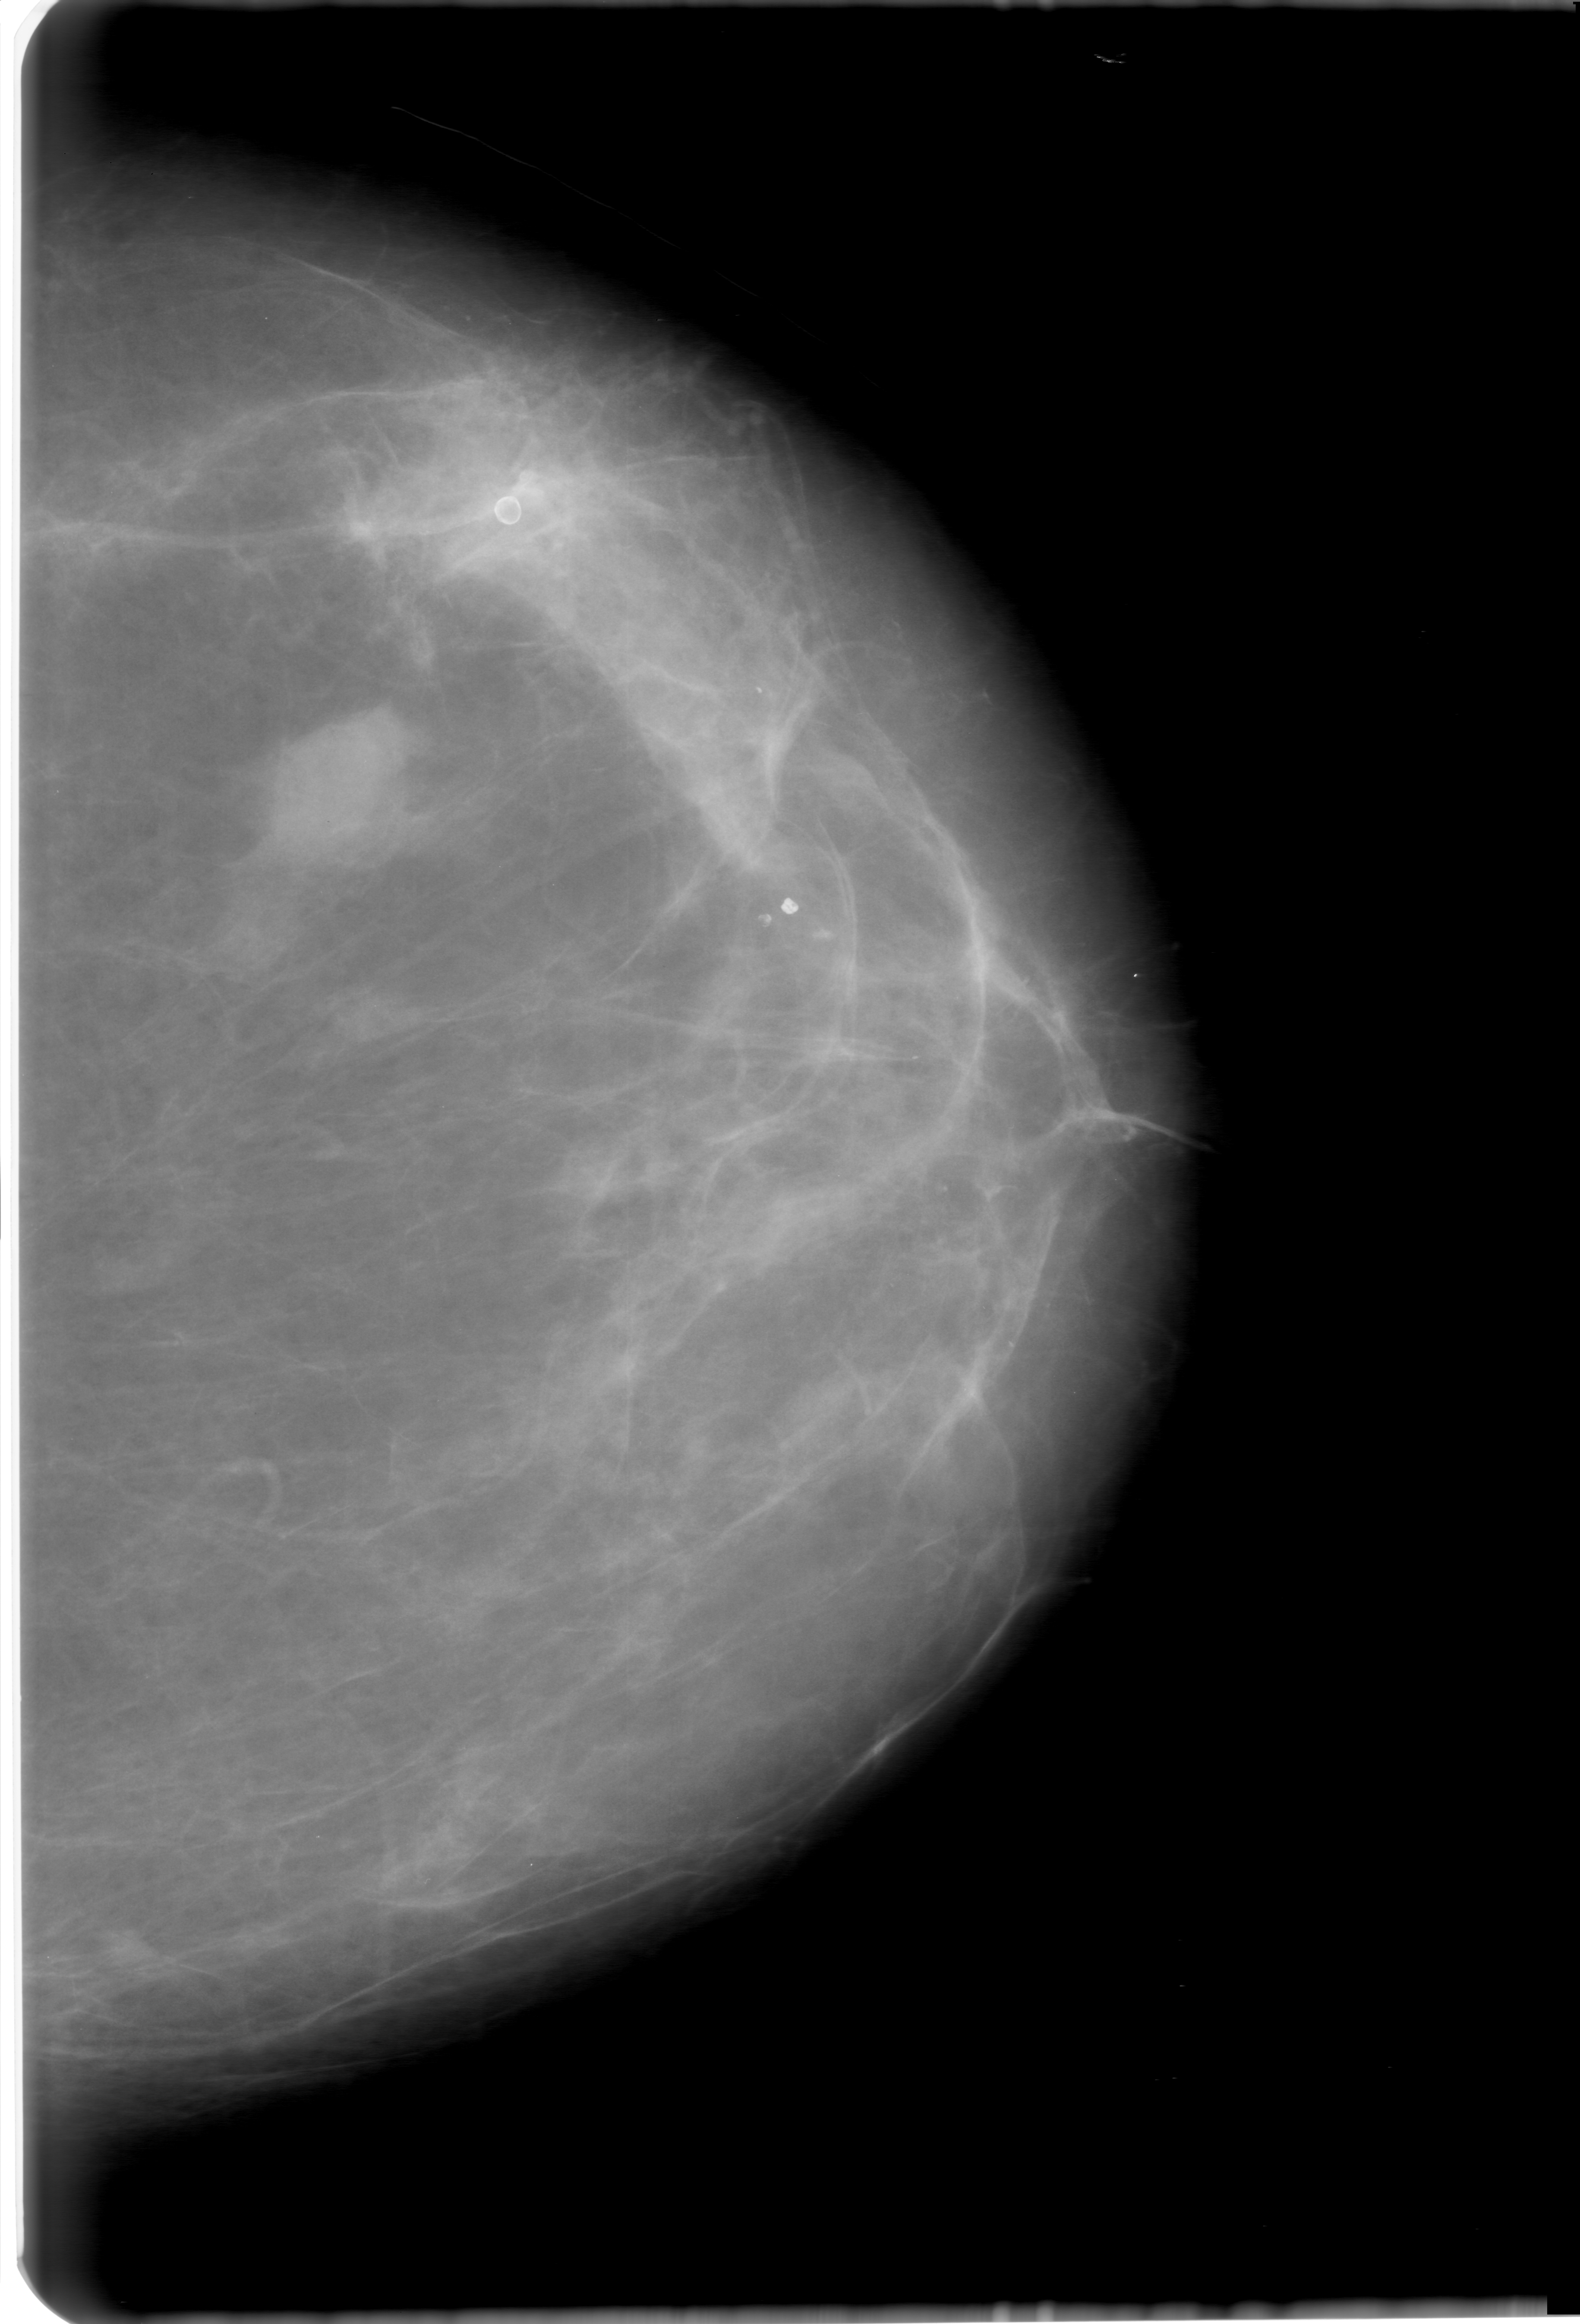
Mammogram (digitized film), left breast, CC view, breast composition: scattered fibroglandular densities (BI-RADS density category 2 of 4).
Marked findings (only marked abnormalities are described; nothing is implied about the rest of the image): mass, shape oval, margins microlobulated; BI-RADS assessment category 0; subtlety rating 5 on a 1 (subtle) to 5 (obvious) scale; pathology (as recorded): benign.